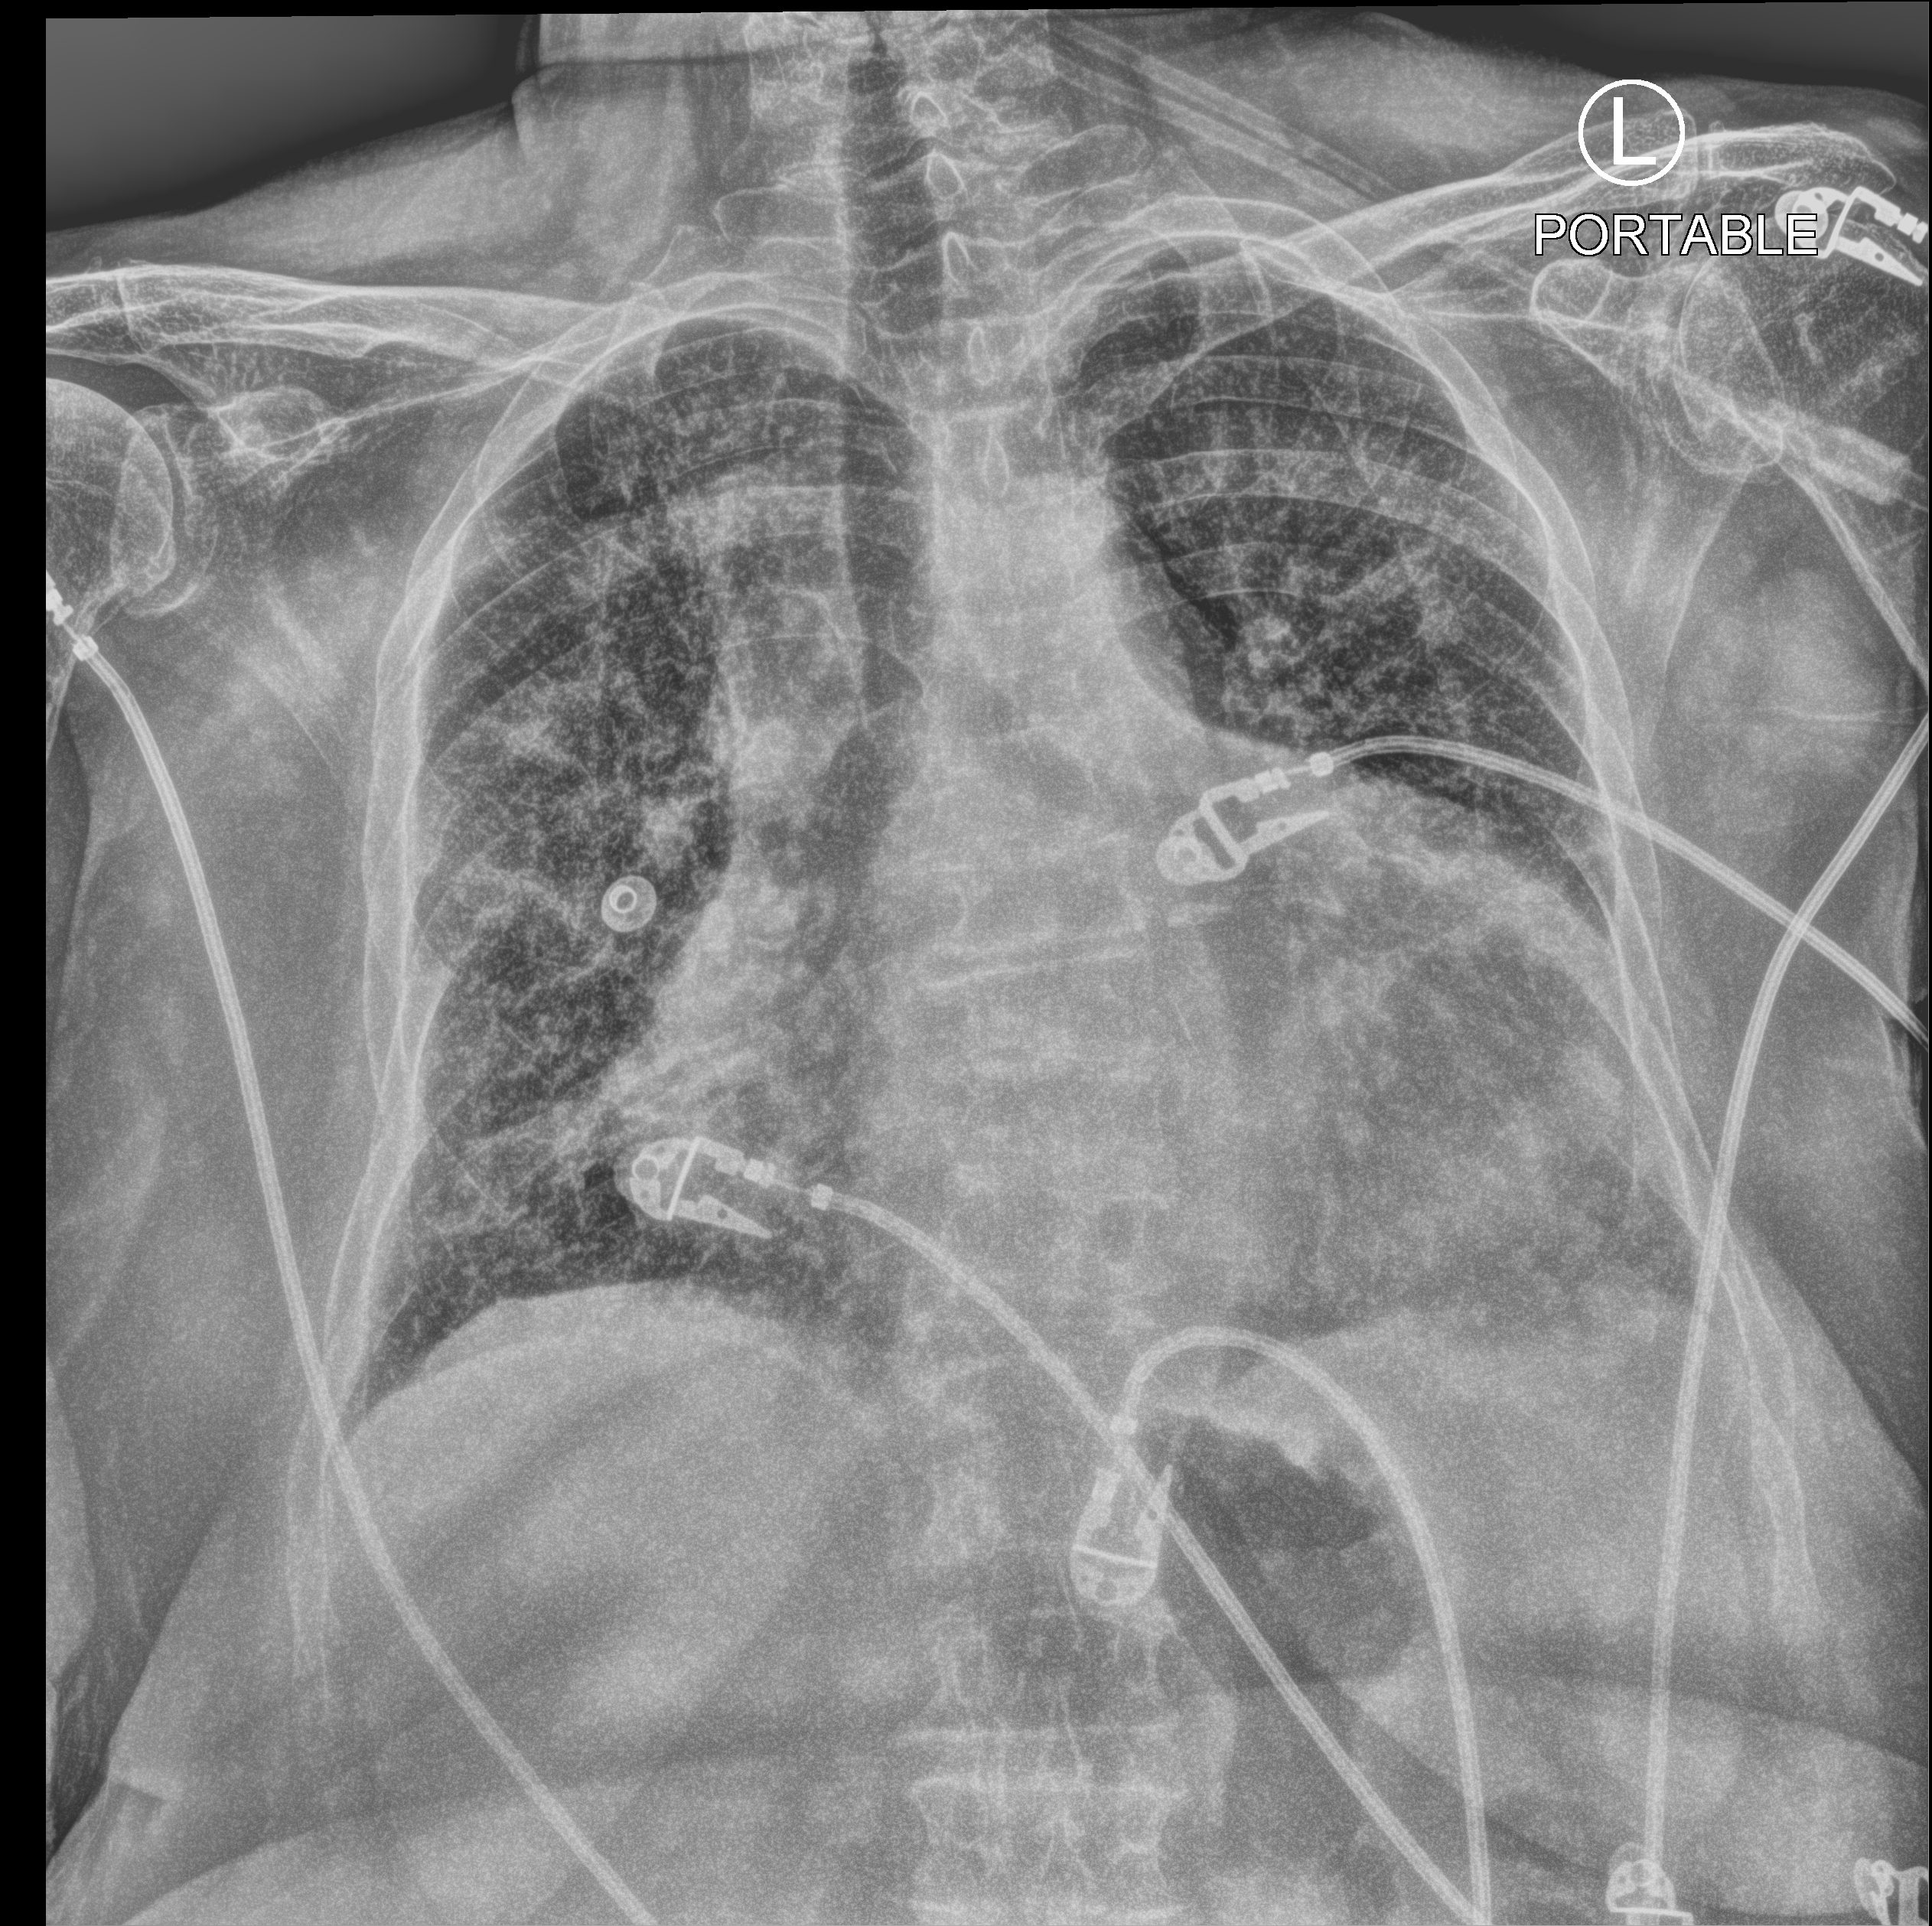
Bedside chest radiograph (computed radiography), anteroposterior (AP) projection. Patient hospitalised with COVID-19; female, aged 75–90 years.
Admission-level facts for this patient (not findings on this image; timing relative to this image not recorded): hypertension (admission record): yes.